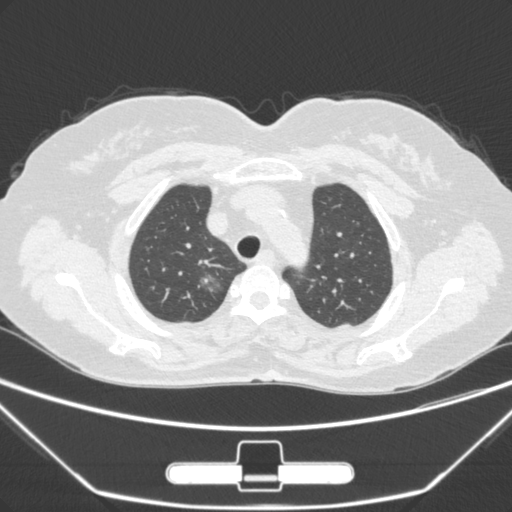
Chest CT, one axial slice. Position 227 of 275 along the scan axis. 120 kVp. Lung window (W 1500 / L -600 HU). 1 mm slice thickness. 512 × 512 image matrix. Female patient, age 63 years. From the clinical record (not read from this slice): clinical TNM (as recorded): T1a N0 M0; histopathological grade: G1.
Outlined on this slice (rectangle marked by the reading radiologist):
- lung tumour (recorded histology: adenocarcinoma): box from (x=190, y=265) to (x=235, y=306) px